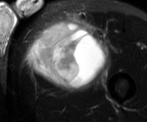
MRI of an extremity soft-tissue mass, one axial slice. Position 42 of 52 along the scan axis. T2-weighted fat-saturated. MR volume resampled by the dataset authors to the PET/CT grid (not the native acquisition matrix). 3.27 mm slice thickness. 147 × 122 image matrix. Male patient. From the clinical record (not read from this slice): histological type: pleiomorphic liposarcoma; grade: high; site of the primary tumour: left thigh.
Structures marked on this image (expert contour drawn on MRI and transferred to this co-registered scan by the dataset authors):
- gross tumour volume including surrounding oedema: box from (x=32, y=16) to (x=106, y=83) px
- gross tumour volume (mass): (x=32, y=25)–(x=101, y=83)